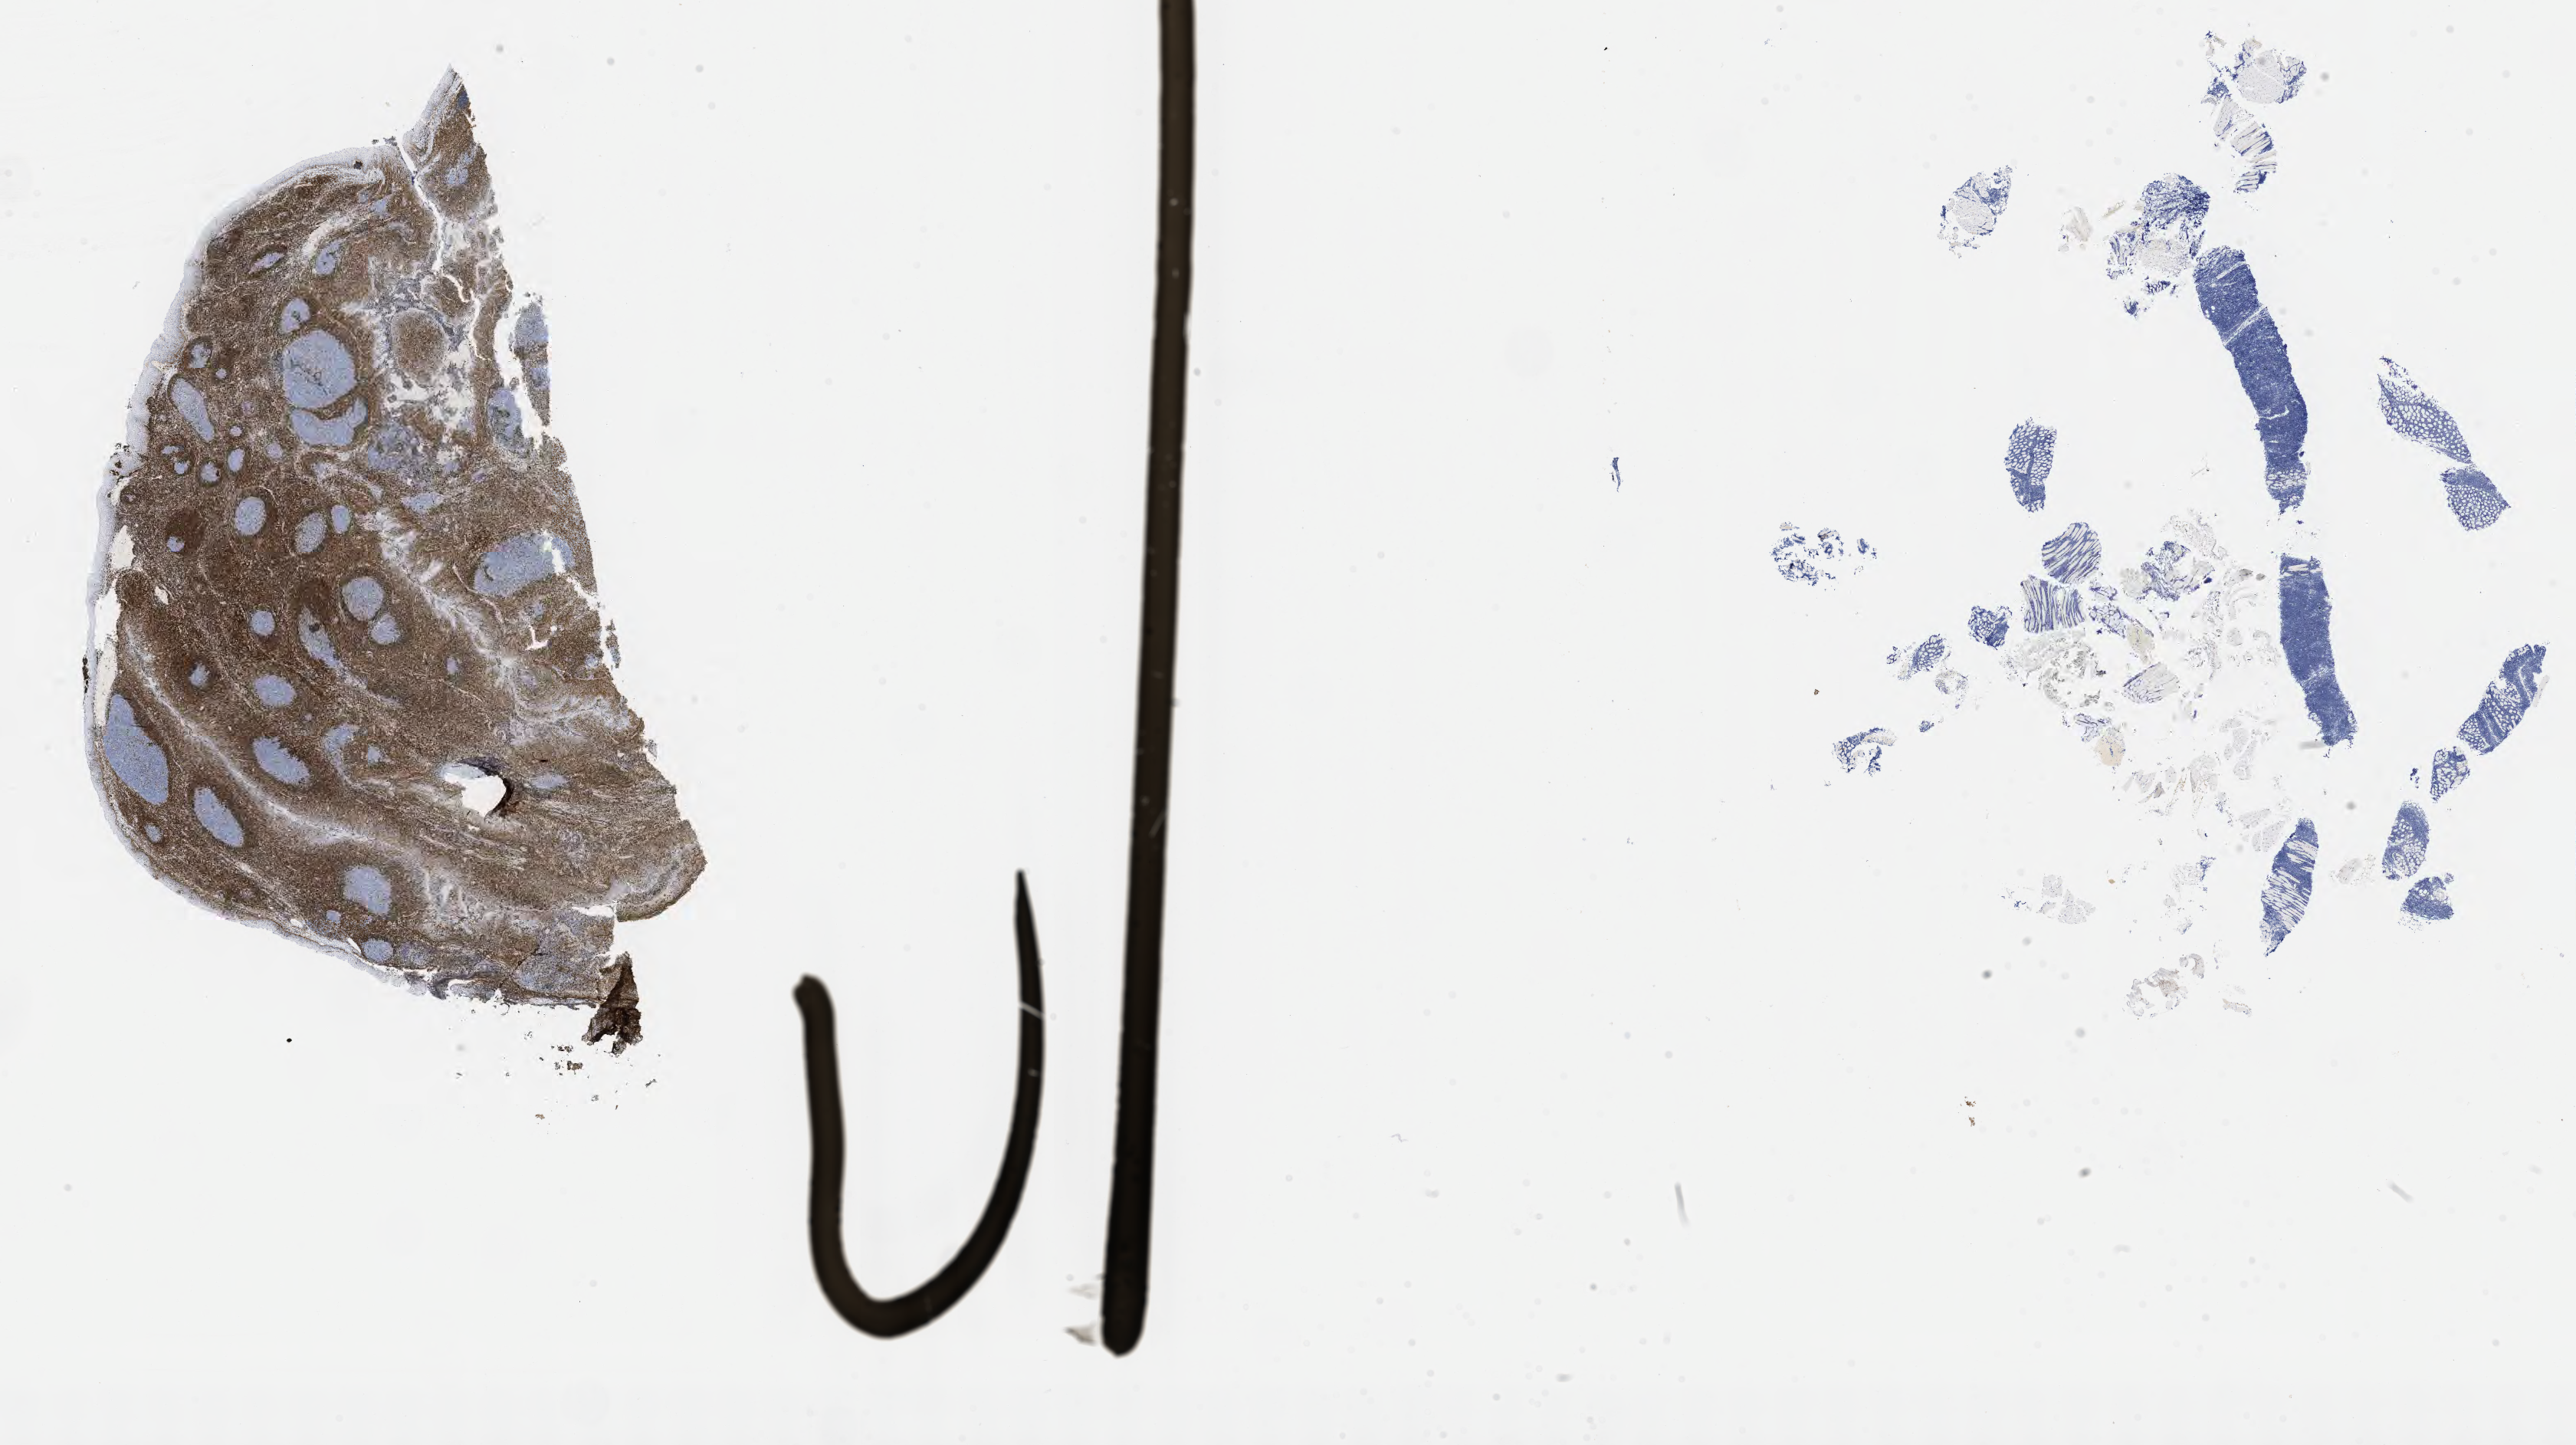
Immunohistochemistry (IHC) whole-slide image stained for BCL2 — whole scanned area (about 27.2 x 15.2 mm) shown as a low-resolution overview. Specimen: tumor tissue. Anatomic site: retroperitoneum. Patient female; 53 years old.
Diagnosis: Burkitt lymphoma, NOS.